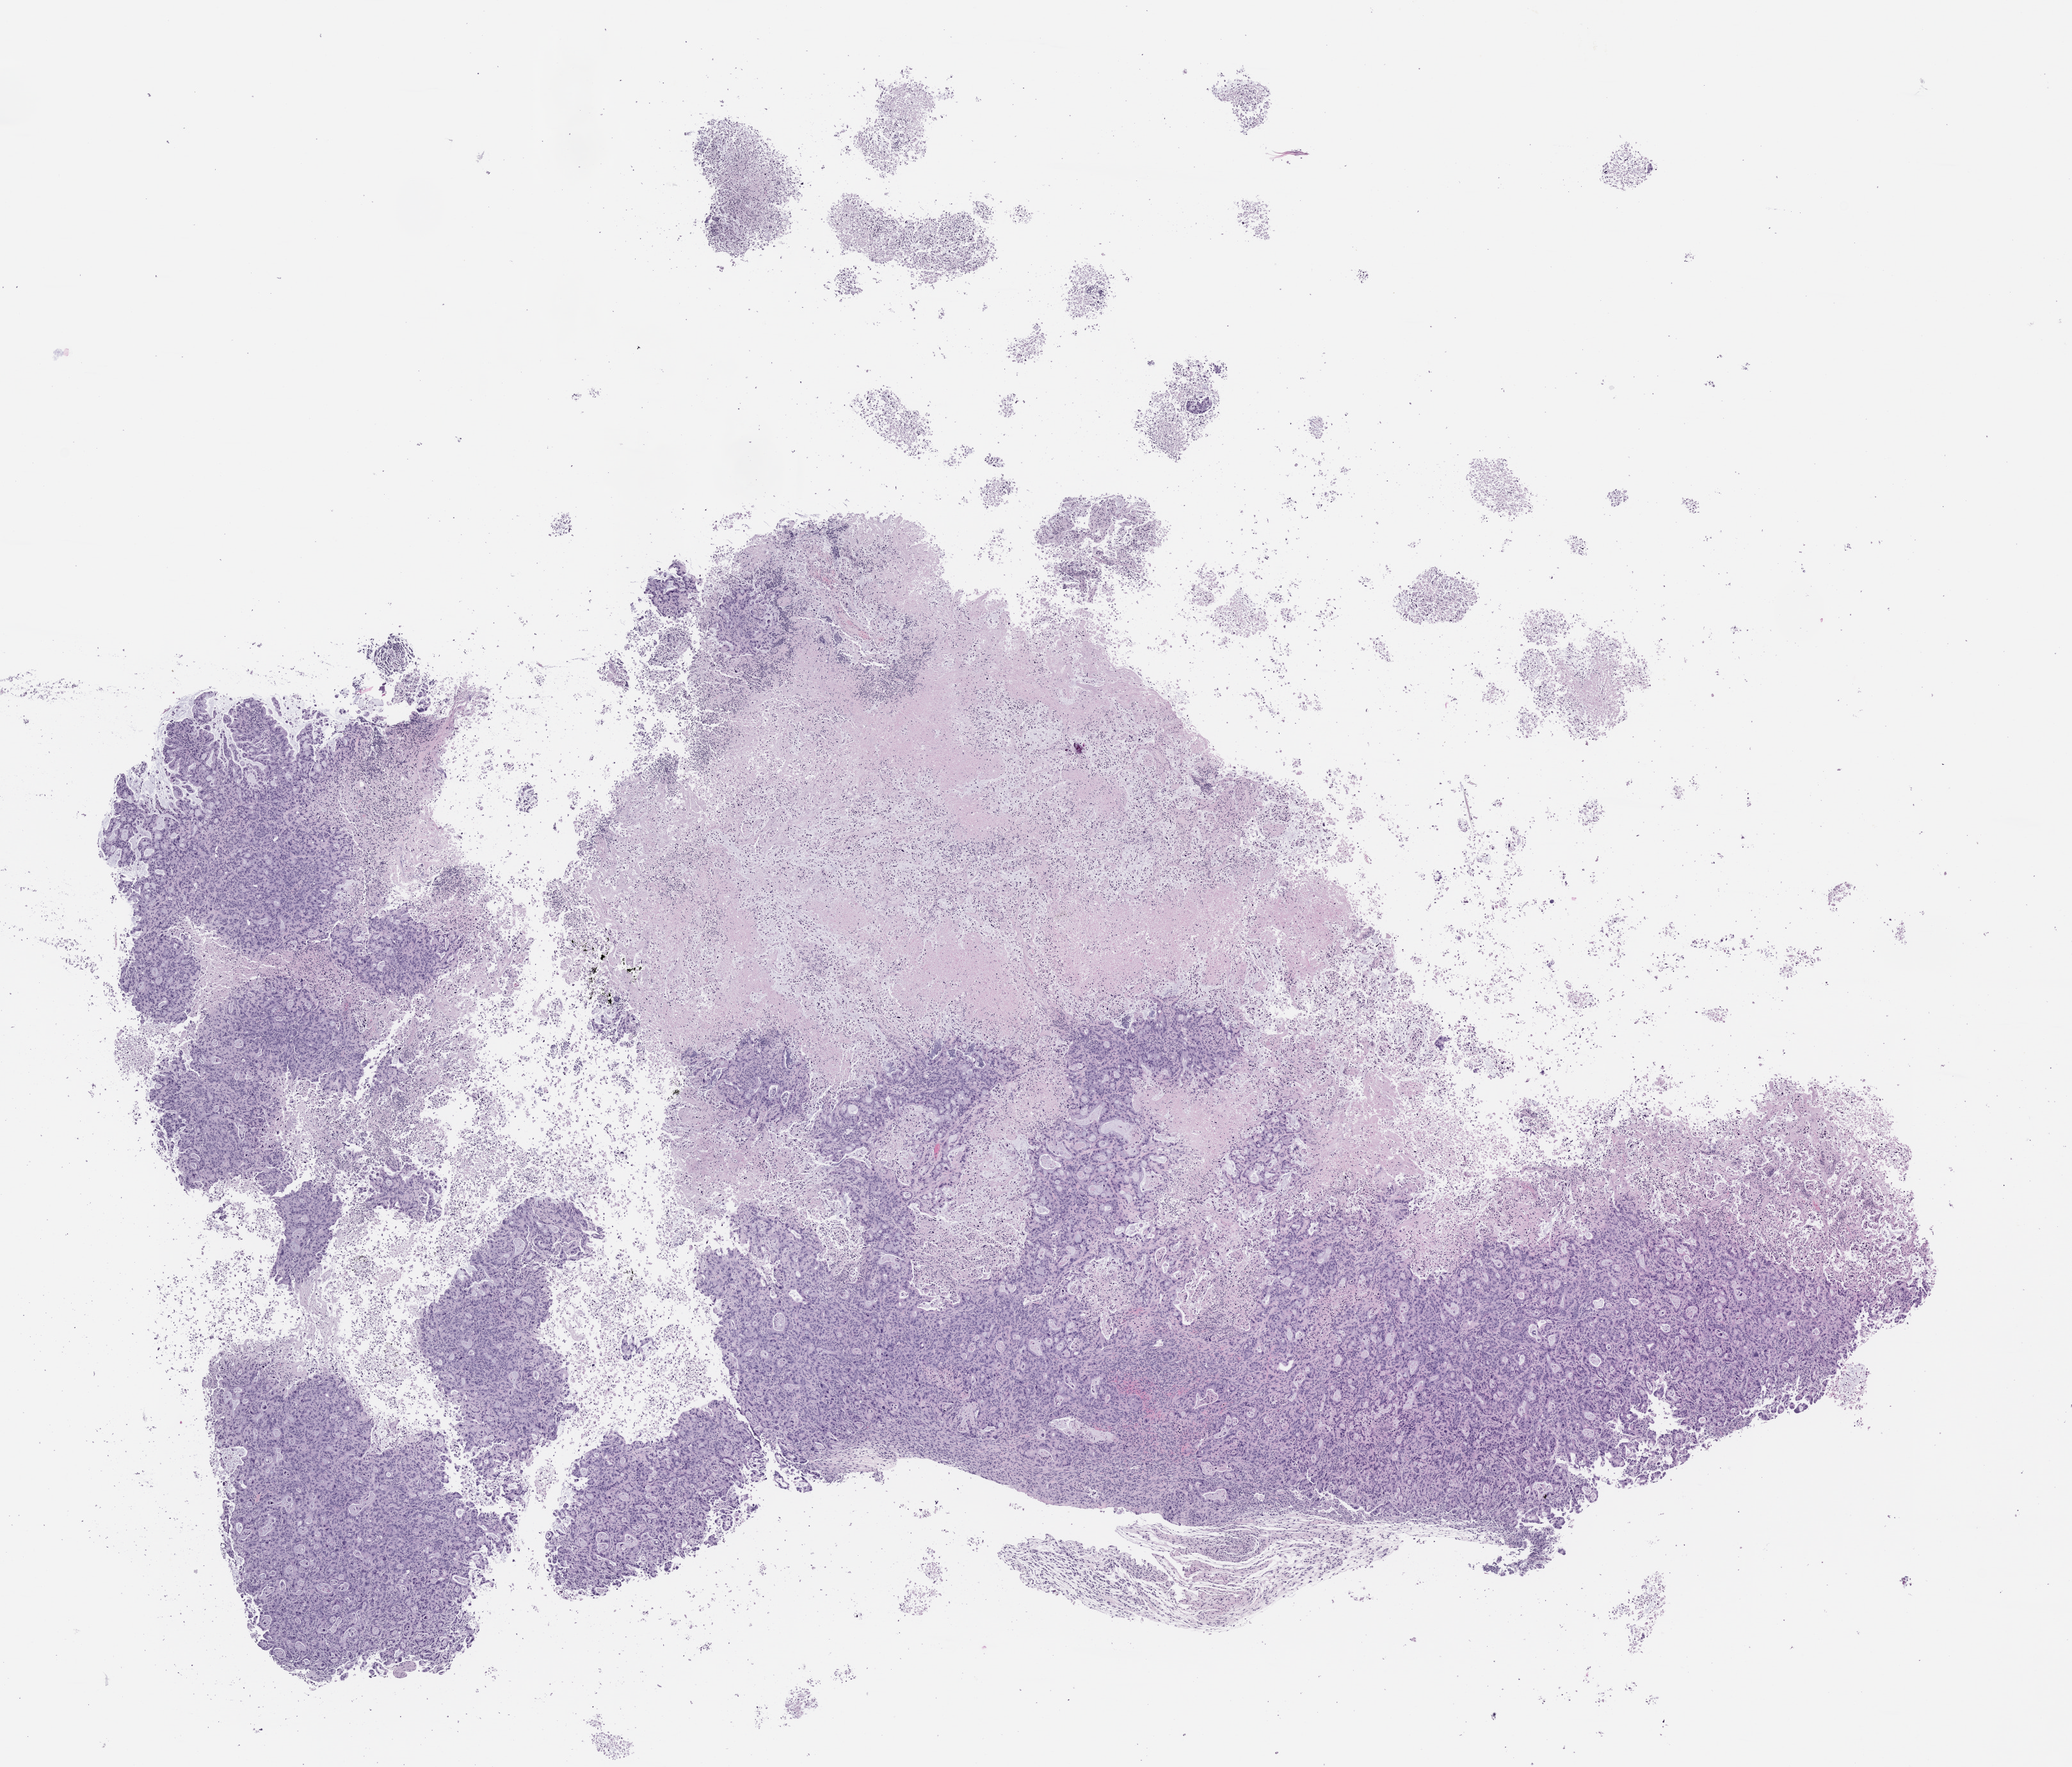
H&E whole-slide image of a patient-derived xenograft (PDX) tumor grown in a mouse, passage 1, a low-resolution overview of the entire scanned area, about 13.0 x 11.1 mm, FFPE section, originating tumor site category: pancreas.
Originating patient diagnosis: Pancreatic Adenocarcinoma.